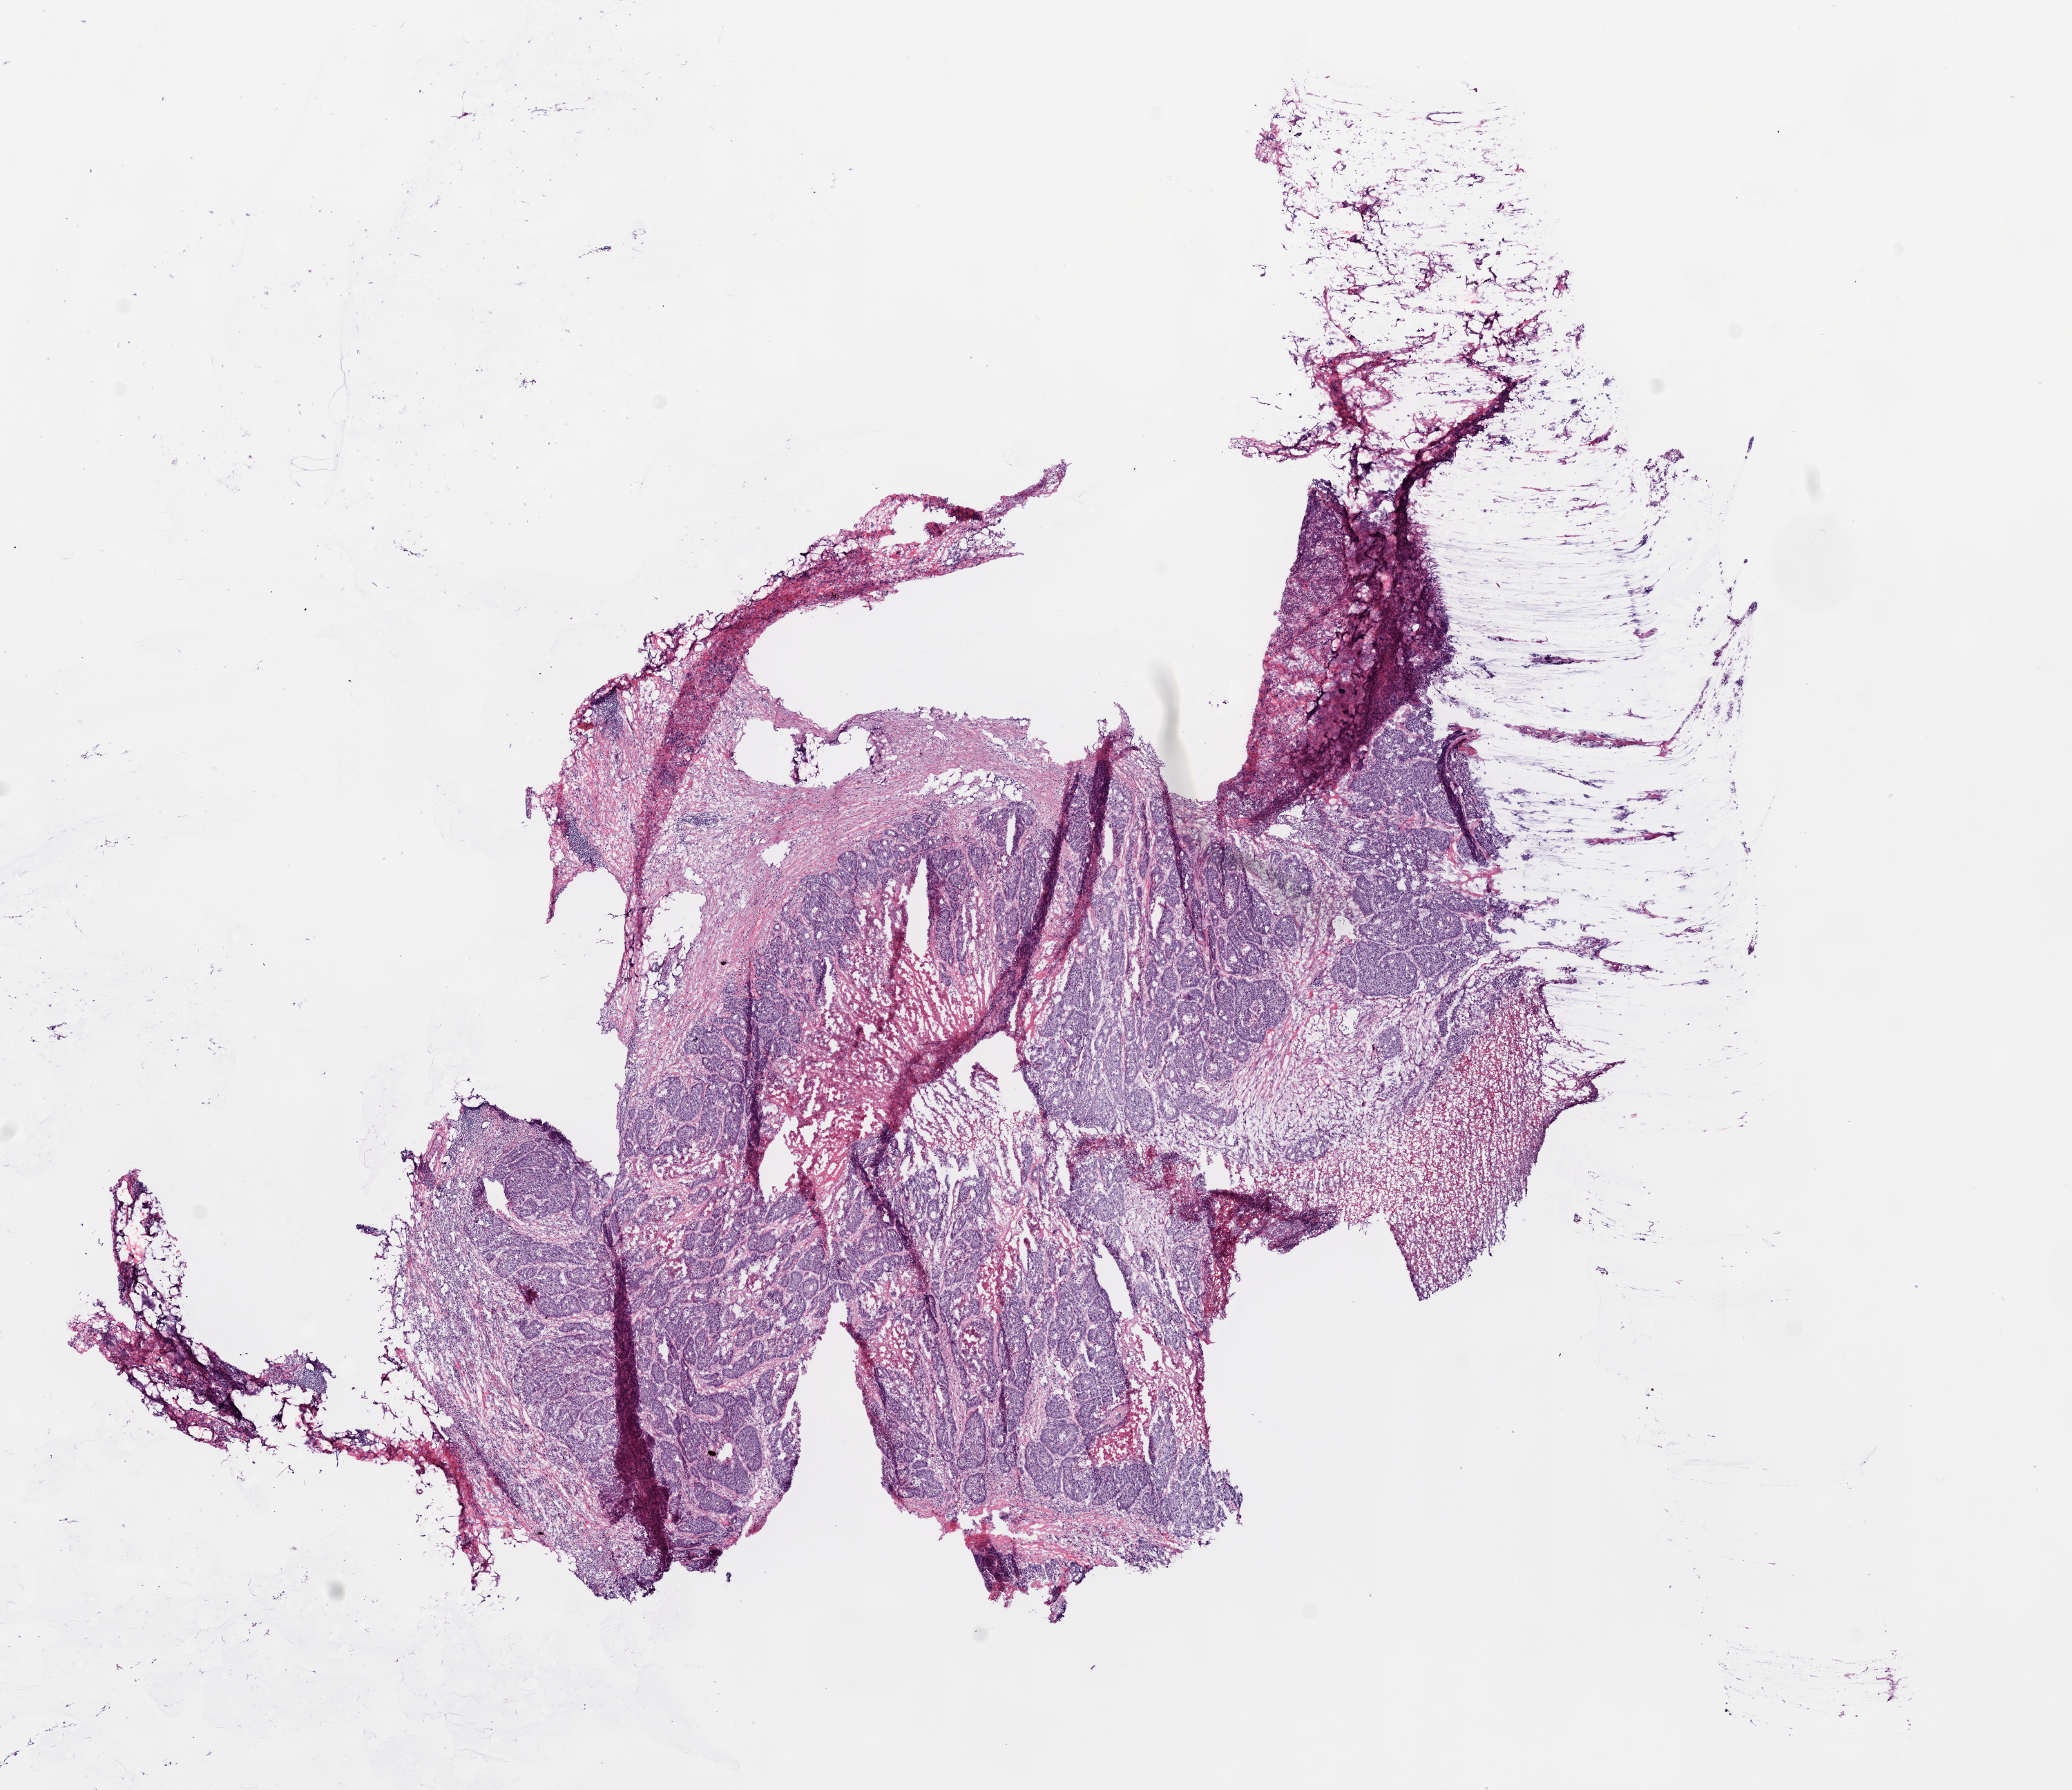
Whole-slide histology image, H&E-stained, low-resolution overview of the scanned area, about 12.0 x 10.4 mm (acquisition: 20x scan). Frozen section. Sample: primary tumour, colon. Male patient; age at initial diagnosis 75 years. Composition of this section per pathologist review: tumour cells 60%, tumour nuclei 80%, normal cells 15%, stromal cells 5%, necrosis 20%.
Diagnosis: Adenocarcinoma, NOS. AJCC pathologic stage: II. TNM: T3 N0 M0. Lymph nodes positive (case pathology): 0 of 28 examined.